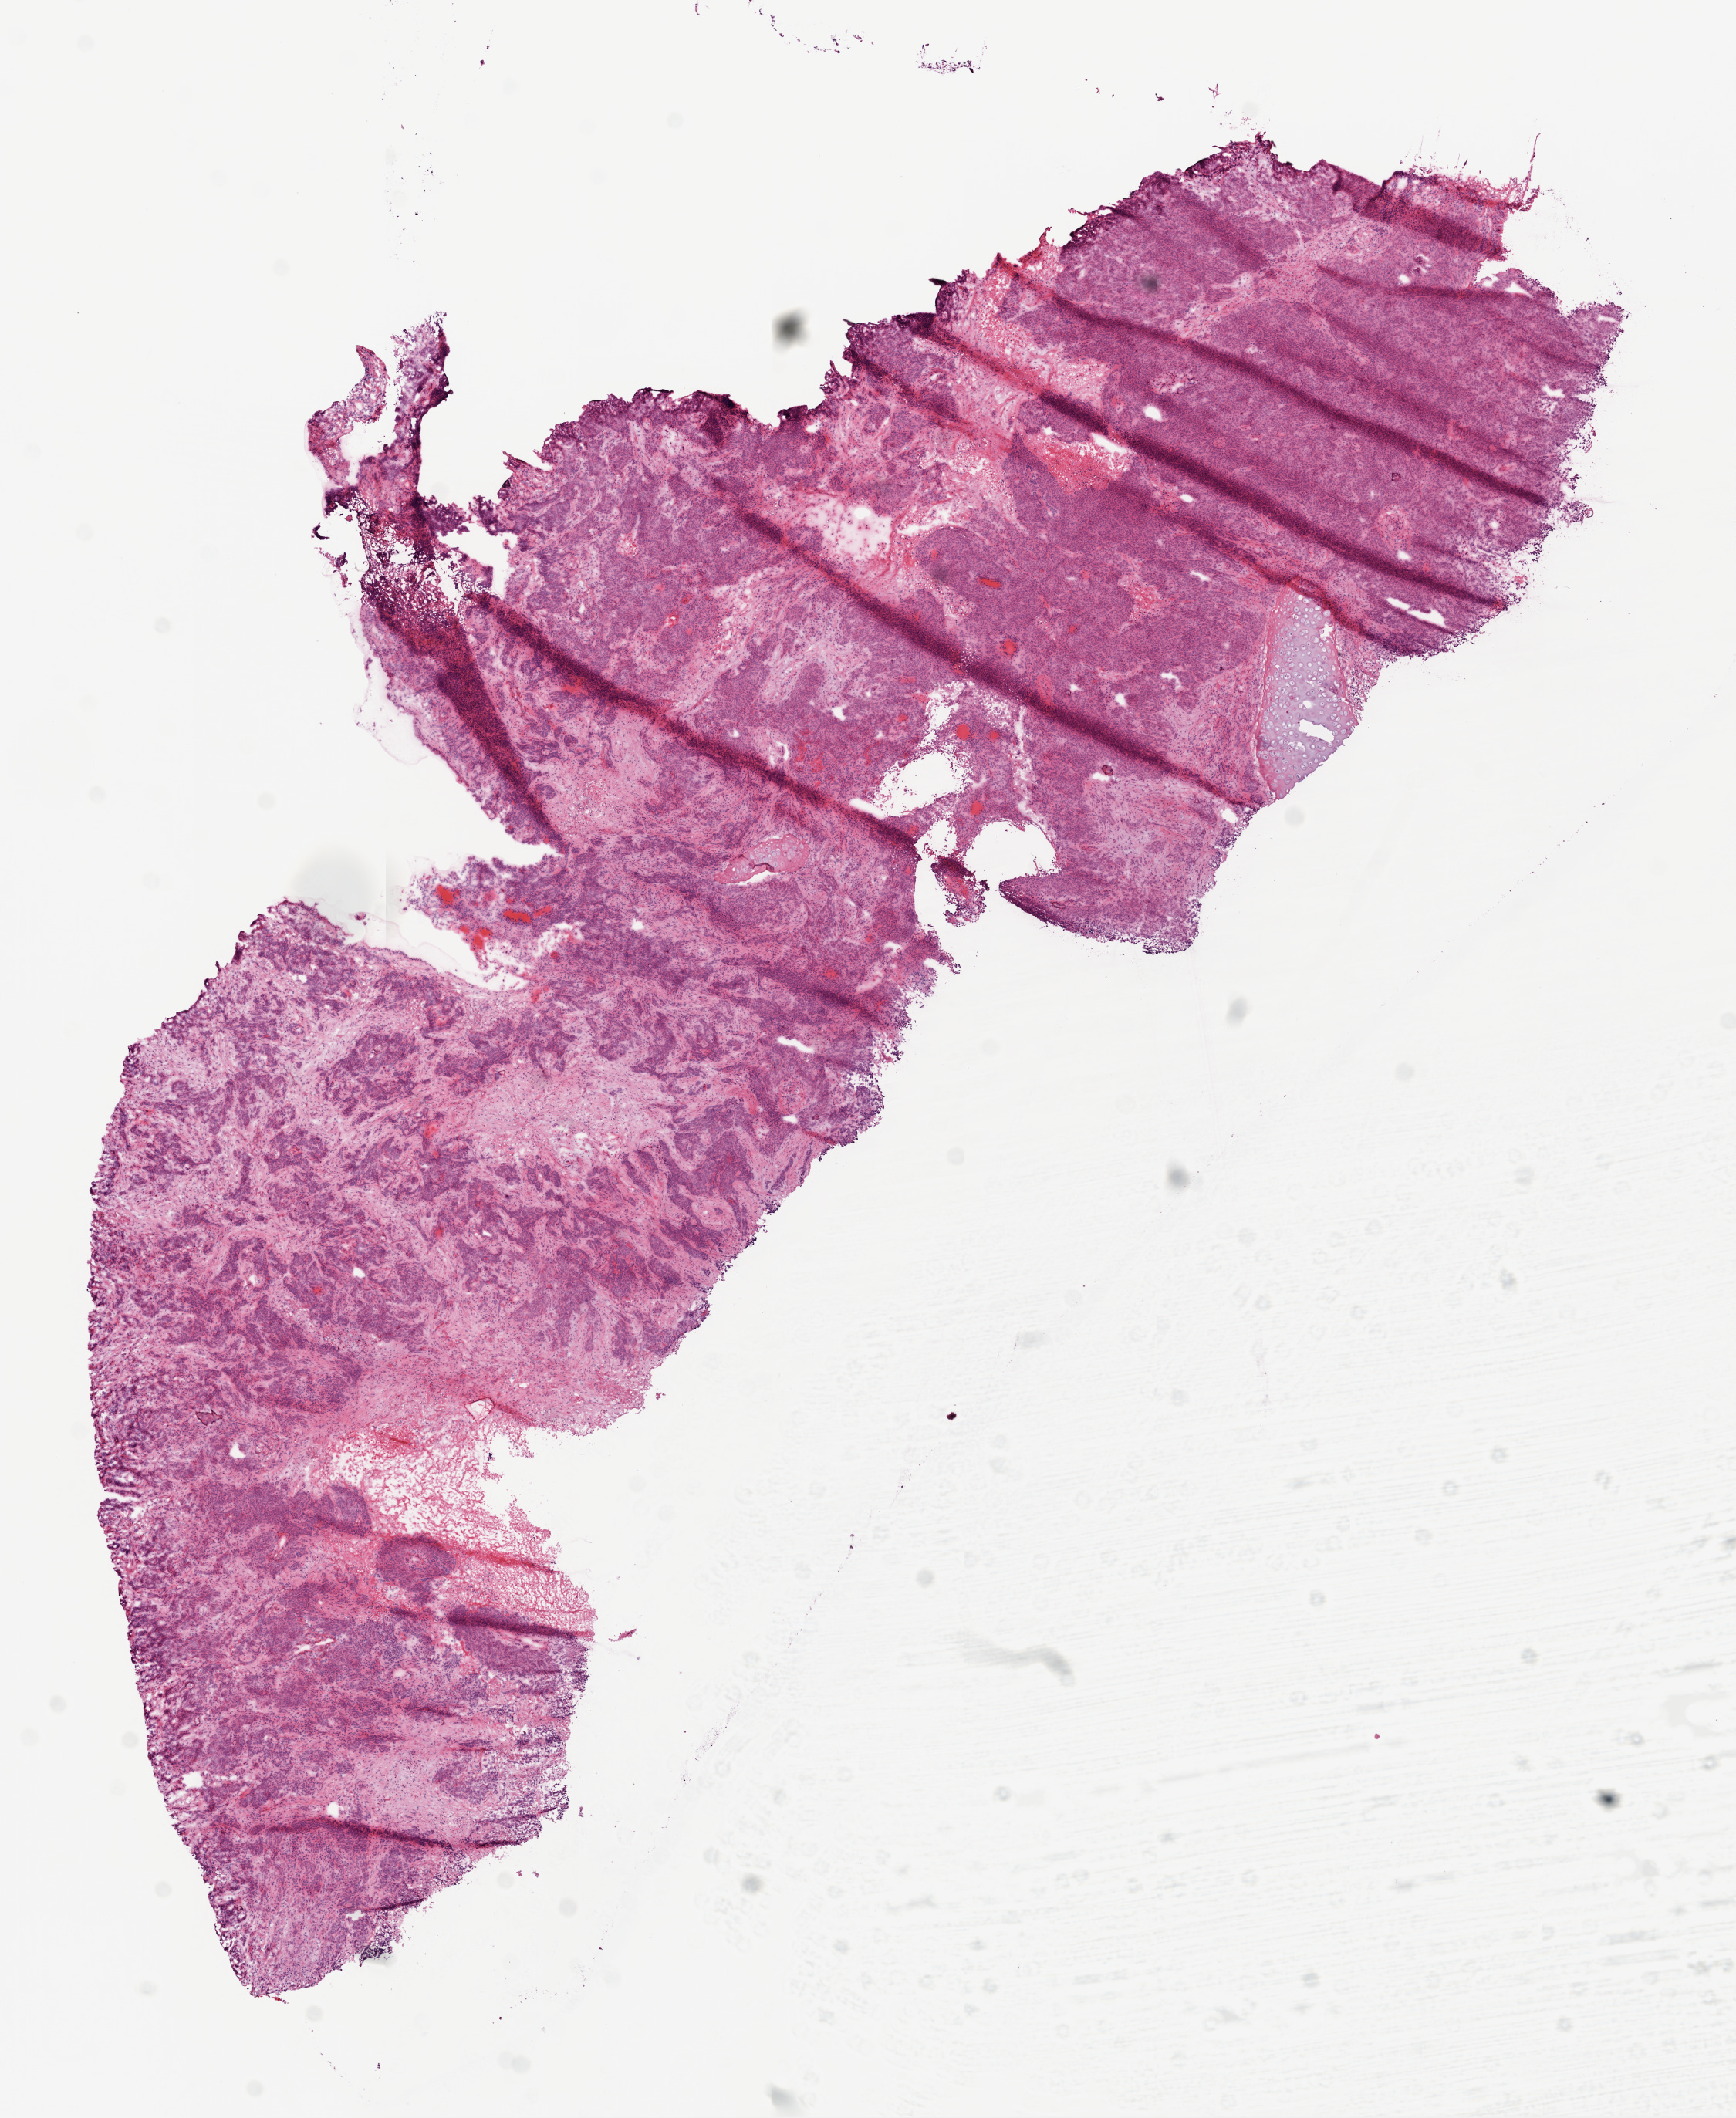
Digitized Hematoxylin and eosin (H&E) stained tissue section (whole slide) — a low-resolution overview of the entire scanned area, about 9.0 x 11.0 mm, frozen section from the top of the tissue portion, sample: primary tumour, lung. Patient: female, age at initial diagnosis 66 years. Pathologist review of this section (percent, as recorded): tumour cells 95%, tumour nuclei 80%, normal cells 0%, stromal cells 0%, necrosis 5%. Infiltration values recorded for this section: lymphocyte infiltration 10%, monocyte infiltration 1%, neutrophil infiltration 2%.
- laterality: left
- AJCC pathologic stage: IA
- histologic diagnosis: Squamous cell carcinoma, NOS (upper lobe, lung)